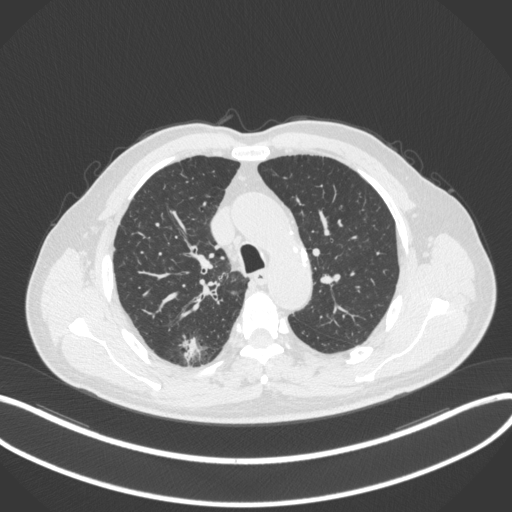
Chest CT, one axial slice. Slice 269 of 366 in the series (ordered by position). Reconstruction kernel B31f. 120 kVp. Lung window (W 1500 / L -600 HU). 1 mm slice thickness. 512 × 512 image matrix, field of view 400 × 400 mm. Patient: male, 69 years. Case-level facts recorded for this patient, not image findings: clinical TNM (as recorded): T1b N0 M0; histopathological grade: G2-3.
Annotated regions visible in this slice (rectangle marked by the reading radiologist):
- lung tumour (recorded histology: adenocarcinoma): box from (x=177, y=336) to (x=203, y=364) px